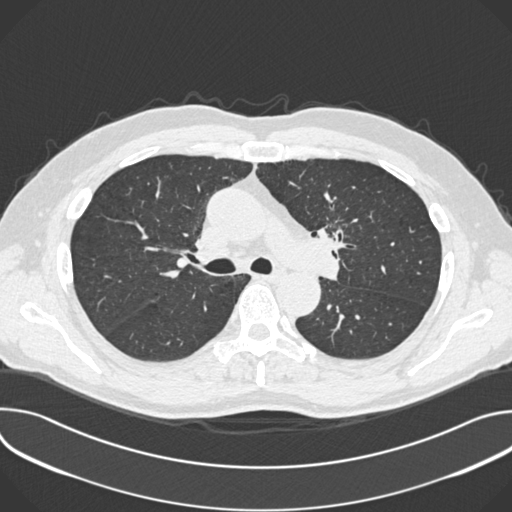
Low-dose screening chest CT, one axial slice. Position 242 of 361 along the scan axis. Reconstruction kernel B30f. 120 kVp. Lung window (W 1500 / L -600 HU). 512 × 512 image matrix, field of view 380 × 380 mm.
Structures marked on this image (expert manual segmentation):
- lesion 1 (tumor, upper lobe of left lung): bounding box [x1, y1, x2, y2] px = [317, 228, 346, 252]